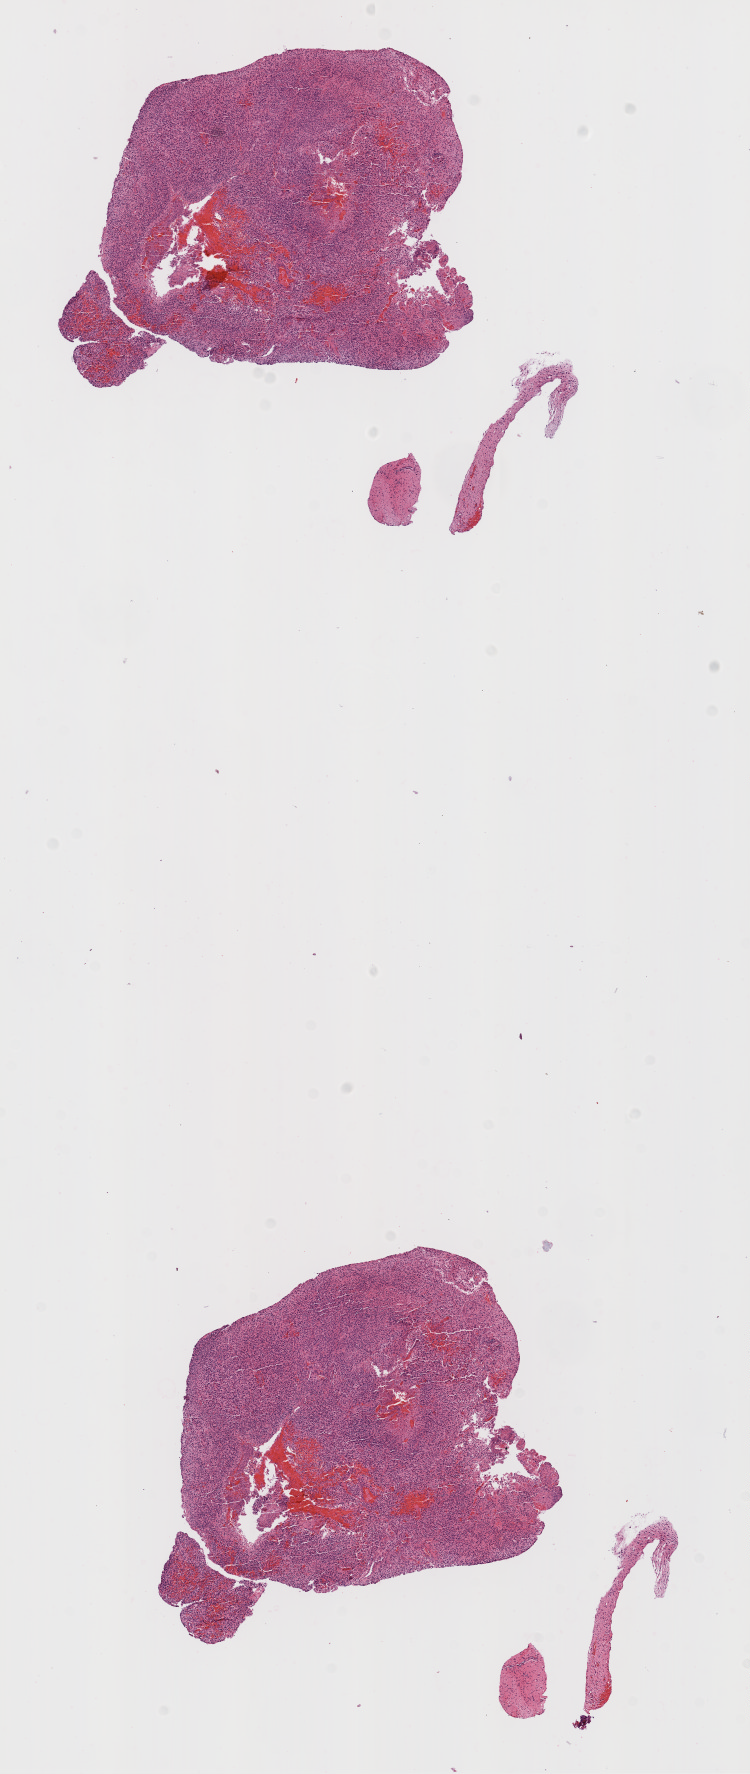
Digitized H&E-stained tissue section (whole slide) — shown as a low-resolution overview of the whole scanned area (about 6.0 x 14.2 mm). Formalin-fixed paraffin-embedded (FFPE) diagnostic section. Primary tumour sample from the brain. Male, age 68 years at initial diagnosis.
Diagnosis: Glioblastoma.